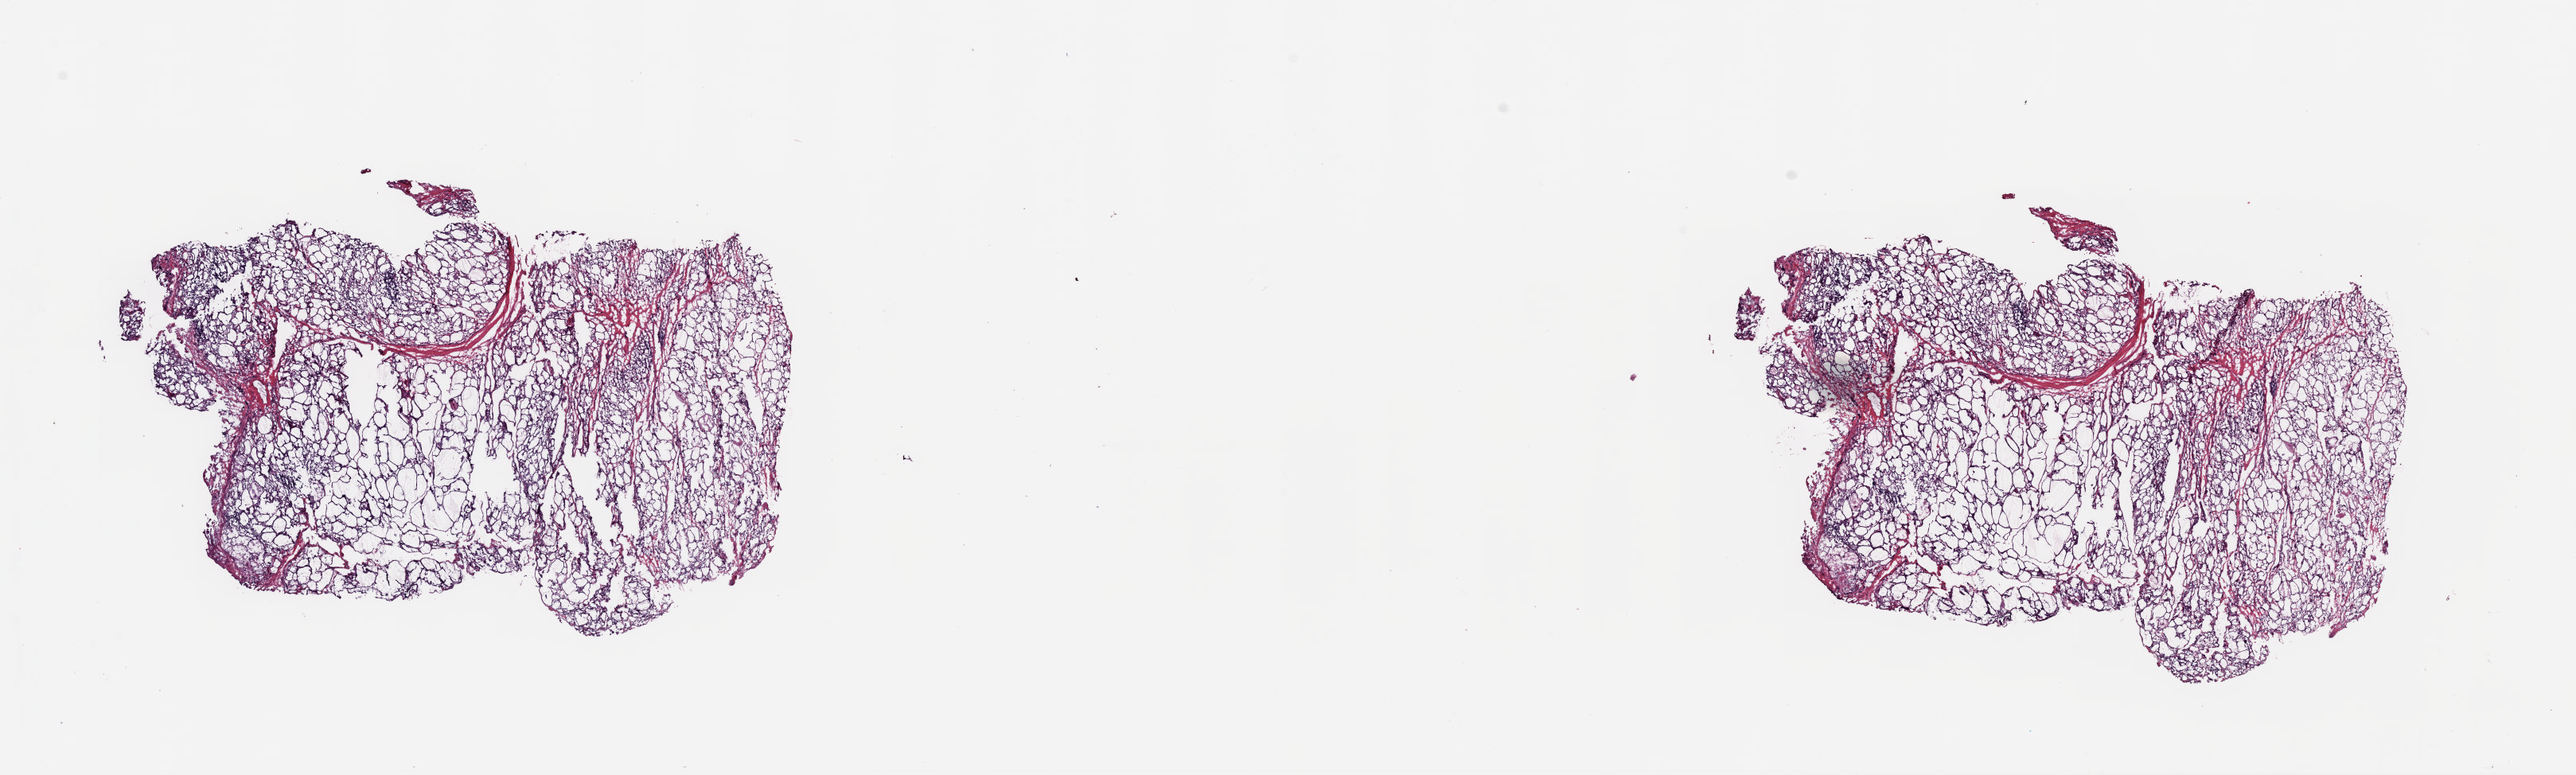
Digitized Hematoxylin and eosin (H&E) stained tissue section (whole slide) — whole scanned area (about 25.6 x 7.7 mm) shown as a low-resolution overview. Frozen section. Thyroid, solid tissue normal (non-tumour tissue) sample. Female, age 34 years at initial diagnosis. Pathologist review of this section (percent, as recorded): tumour cells 0%, tumour nuclei 0%.
This section: solid tissue normal (non-tumour) sample from the same patient. Patient diagnosis: Papillary adenocarcinoma, NOS (thyroid gland).